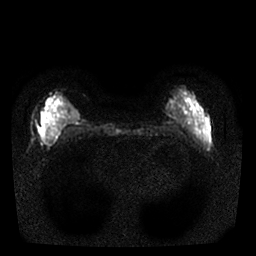
Breast MRI, one axial slice. Slice 6 of 25 in the series (ordered by position). Diffusion-weighted series; image 2 of 4 stored at this slice position (different b-values; order by instance number). 1.5 T. 256 × 256 image matrix, field of view 310 × 310 mm. Female patient.
Annotated regions visible in this slice (manually delineated by an expert):
- tumour on diffusion-weighted imaging: bounding box (x1, y1, x2, y2) in pixels: (39, 115, 47, 143)